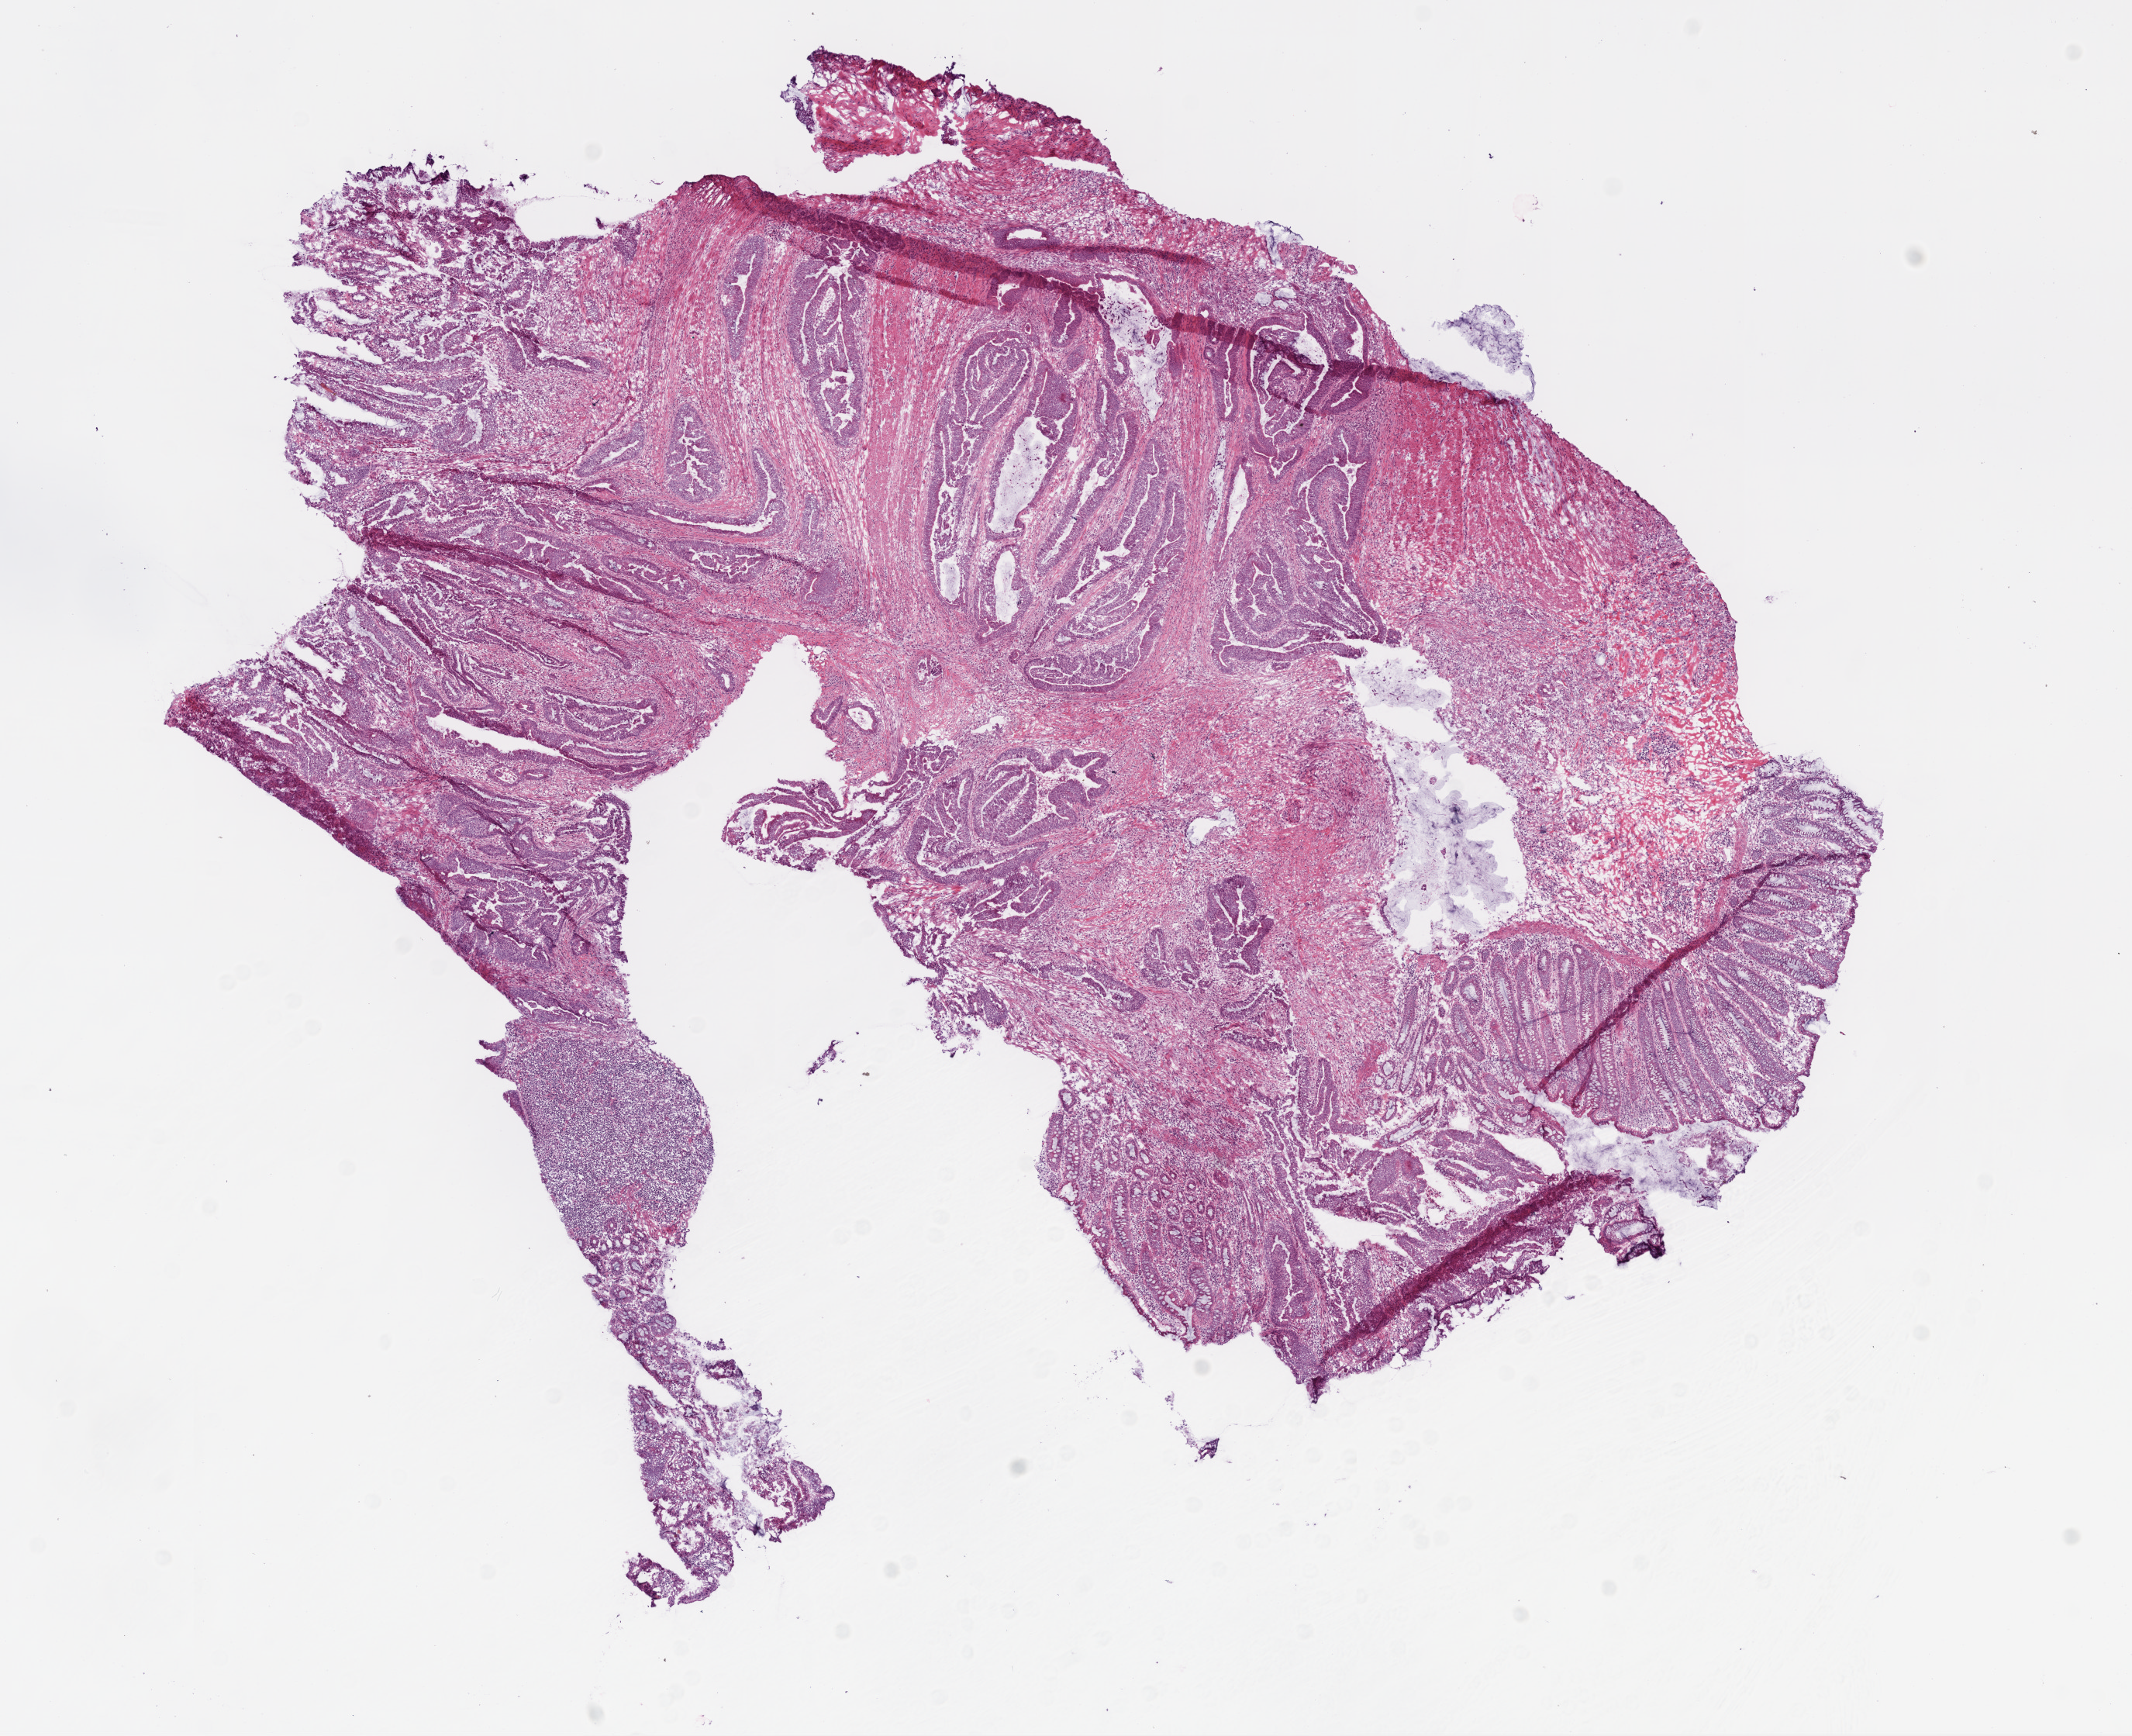
H&E-stained whole-slide image, a low-resolution overview of the entire scanned area, about 11.0 x 9.0 mm, frozen section from the bottom of the tissue portion, sample: primary tumour, colon. Male, age 67 years at initial diagnosis. Pathologist review of this section (percent, as recorded): tumour cells 64%, tumour nuclei 75%, normal cells 8%, stromal cells 25%, necrosis 3%.
Lymph nodes positive (case pathology): 0 of 36 examined. AJCC pathologic stage: IIA (6th edition). Diagnosis: Mucinous adenocarcinoma.